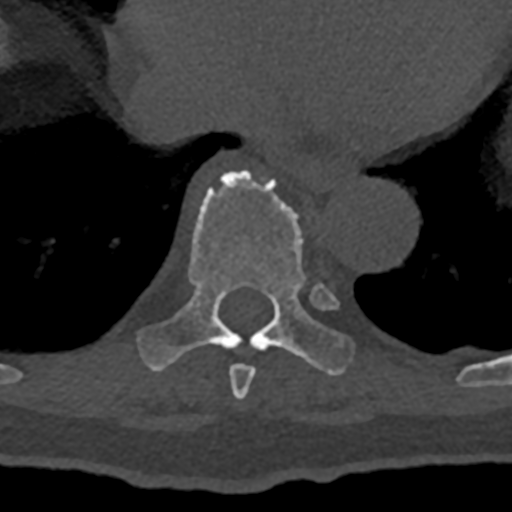
CT including the spine, one axial slice. Slice 665 of 797 in the series (ordered by position). Reconstruction kernel Br40s/3. Bone window (W 1800 / L 400 HU). 0.5 mm slice thickness. 512 × 512 image matrix, field of view 160 × 160 mm. Male patient, age 74 years. Case-level facts recorded for this patient, not image findings: primary cancer: renal; vertebrae with lytic lesions (as recorded): T10, L1, L2, L3, L4, L5.
Annotated regions visible in this slice (semi-automatically segmented with operator editing):
- T8 vertebra: bounding box [x1, y1, x2, y2] px = [229, 364, 255, 399]
- T9 vertebra: [136, 170, 354, 376]